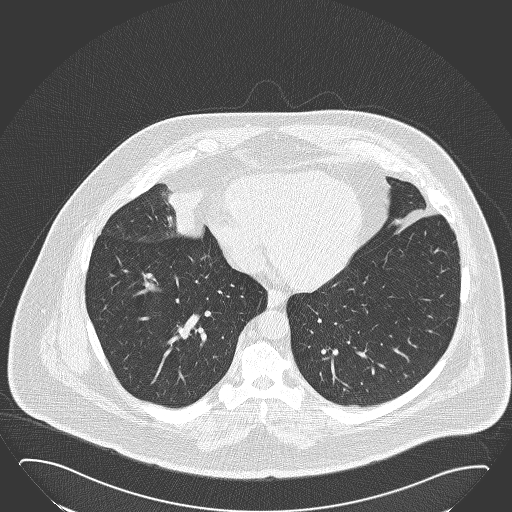
Low-dose screening chest CT, one axial slice; position 60 of 168 along the scan axis; reconstruction kernel B50f; lung window (W 1500 / L -600 HU); 2 mm slice thickness; 512 × 512 image matrix, field of view 432 × 432 mm.
Annotated regions visible in this slice (outlined manually by an expert reader):
- lesion 1 (tumor, hilum of right lung): bounding box <168,188,202,238> (left, top, right, bottom; pixels)